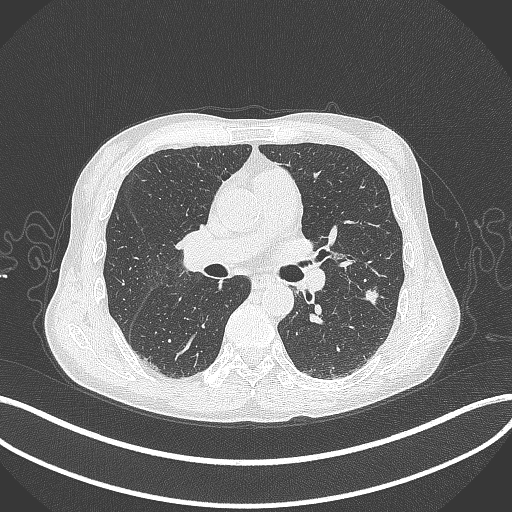
Chest CT, one axial slice. Slice 201 of 429 in the series (ordered by position). Reconstruction kernel B70f. 120 kVp. Lung window (W 1500 / L -600 HU). 1 mm slice thickness. 512 × 512 image matrix, field of view 400 × 400 mm. Male patient, age 58 years. From the clinical record (not read from this slice): clinical TNM (as recorded): T1c N0 M0; histopathological grade: G2.
Annotated regions visible in this slice (bounding box drawn by a radiologist):
- lung tumour (recorded histology: adenocarcinoma): box from (x=363, y=285) to (x=383, y=307) px